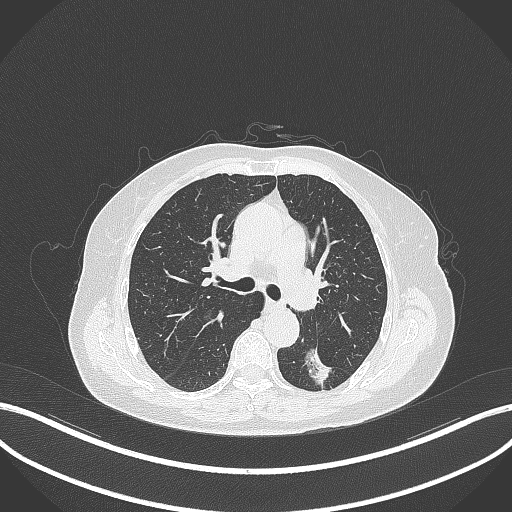
Chest CT, one axial slice. Position 189 of 352 along the scan axis. Reconstruction kernel B70f. 120 kVp. Lung window (W 1500 / L -600 HU). 1 mm slice thickness. 512 × 512 image matrix, field of view 400 × 400 mm. Patient: female, 70 years. Case-level facts recorded for this patient, not image findings: clinical TNM (as recorded): T1c N0 M0.
Outlined on this slice (rectangle marked by the reading radiologist):
- lung tumour (recorded histology: adenocarcinoma): bounding box <300,342,334,390> (left, top, right, bottom; pixels)